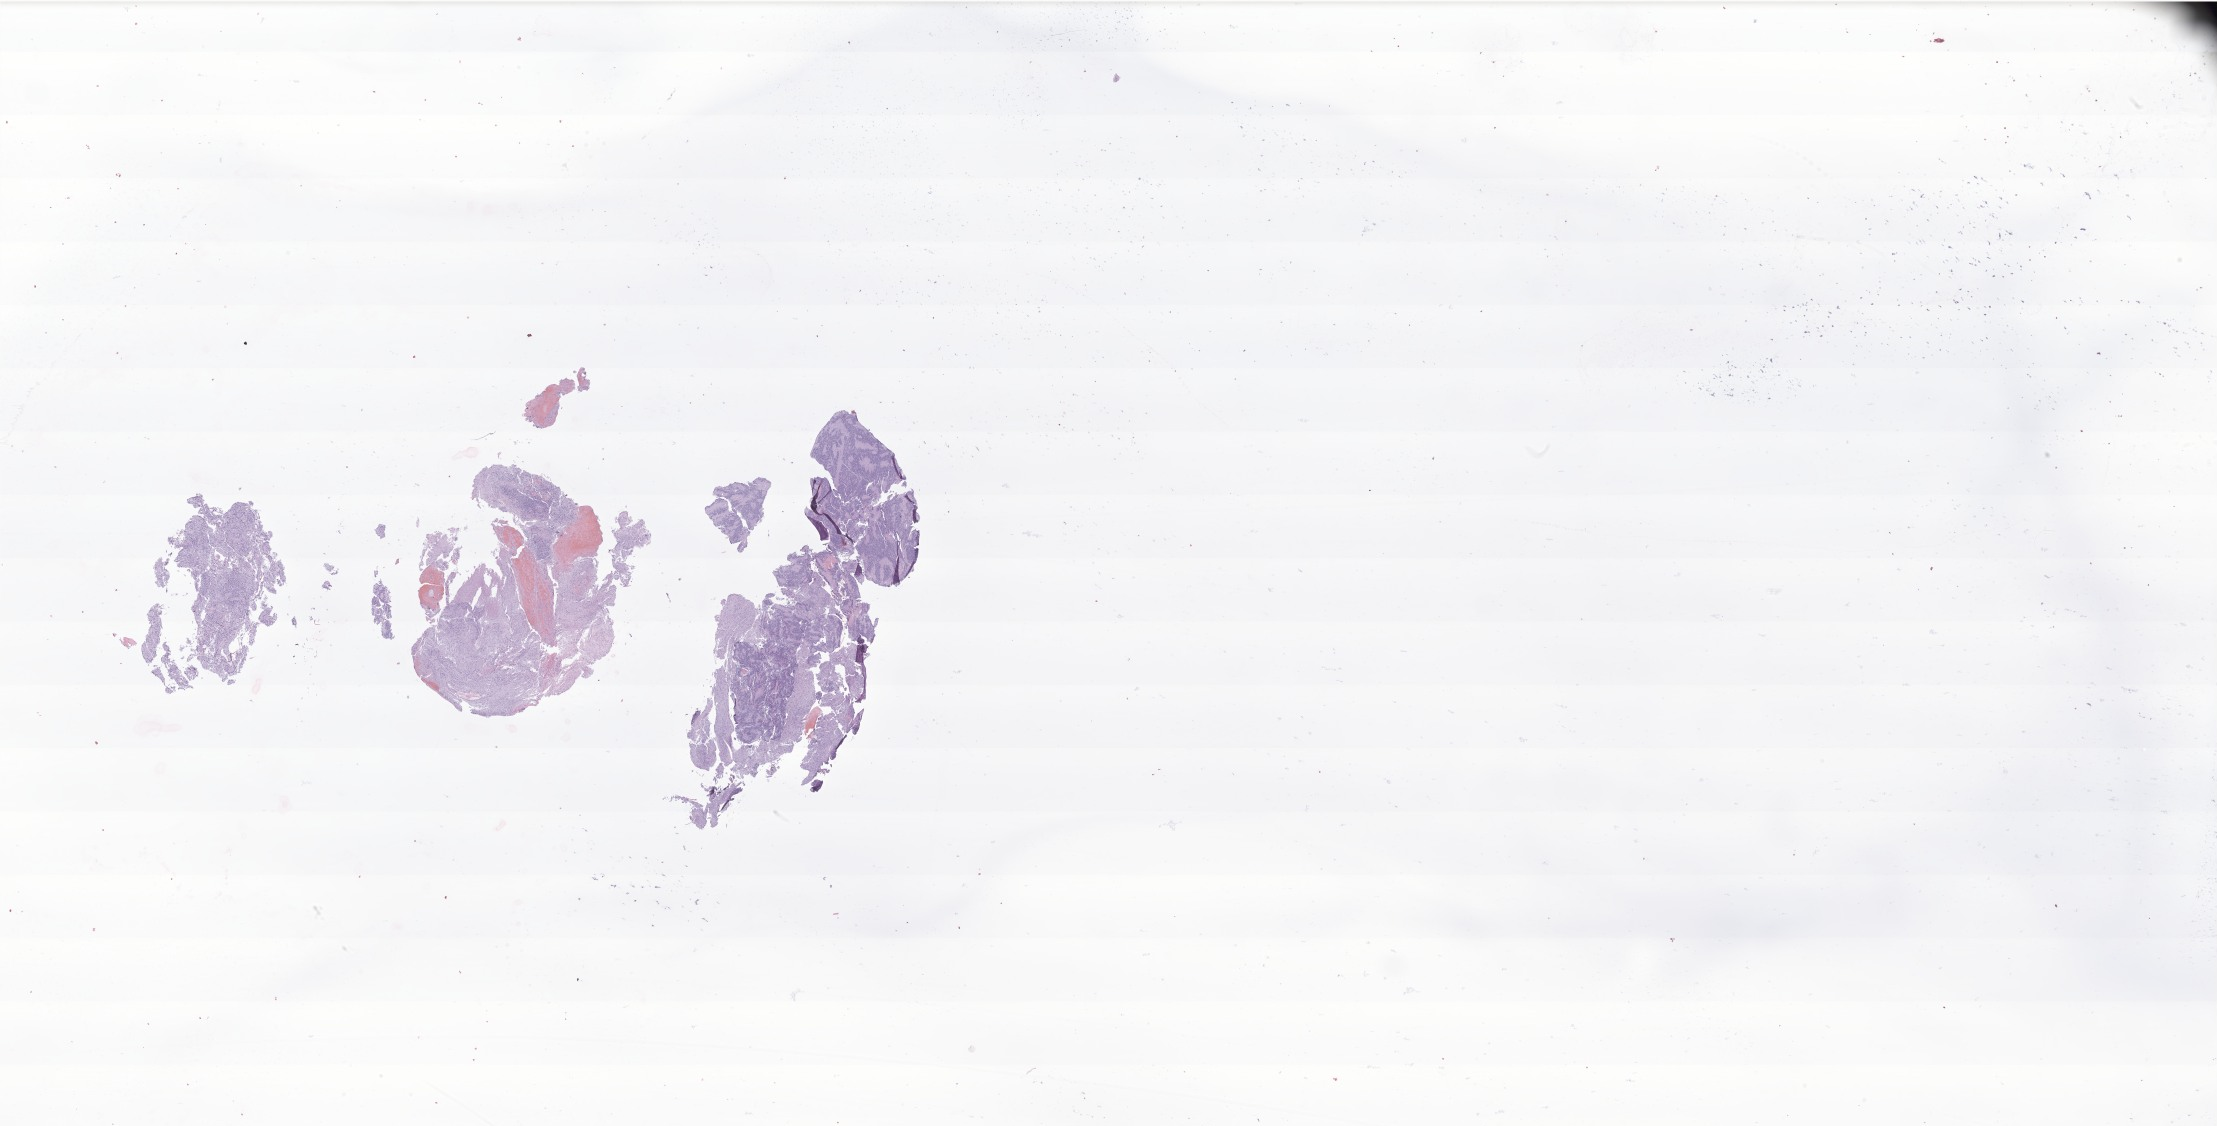
Digitized H&E-stained section of tumor tissue from the brain, whole scanned area (about 37.4 x 19.0 mm) shown as a low-resolution overview; FFPE section. Patient: female, age 820 days (about 2.2 years).
Diagnosis (ICD-O-3 morphology term): Ependymoma, NOS.